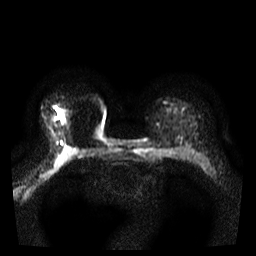
Breast MRI, one axial slice. Slice 25 of 35 in the series (ordered by position). Diffusion-weighted series; image 2 of 4 stored at this slice position (different b-values; order by instance number). 3 T. 5 mm slice thickness. 256 × 256 image matrix, field of view 300 × 300 mm. Female patient.
Outlined on this slice (manually delineated by an expert):
- tumour on diffusion-weighted imaging: bounding box (x1, y1, x2, y2) in pixels: (61, 119, 64, 125)